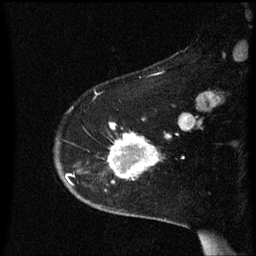
Breast MRI (dynamic contrast-enhanced), one sagittal slice. Position 44 of 60 along the scan axis. Dynamic contrast-enhanced series, image 2 of 3 at this slice position (ordered by acquisition). 1.5 T. TE 4.2 ms, TR 8.4 ms. 256 × 256 image matrix, field of view 200 × 200 mm. Patient: female, 54 years. Case-level facts recorded for this patient, not image findings: setting: breast cancer imaged before/during neoadjuvant chemotherapy; receptor status: HR-positive, HER2-negative.
Structures marked on this image (semi-automatic segmentation, software-assisted and operator-edited):
- analysis volume of interest (the breast-tissue region the enhancement analysis was run in; not a lesion): box from (x=103, y=124) to (x=171, y=183) px
- tumour enhancement mask (voxels above the 70 % enhancement threshold inside the analysis volume of interest): (x=109, y=124)–(x=170, y=179)